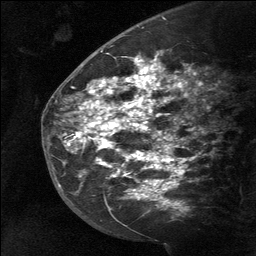
Breast MRI (dynamic contrast-enhanced), one sagittal slice; position 41 of 64 along the scan axis; dynamic contrast-enhanced study with each time point stored as its own series, time point 2 of 3 at this slice position (early post-contrast, ordered by acquisition time); 1.5 T; TE 4.8 ms, TR 27 ms; 2 mm slice thickness; 256 × 256 image matrix, field of view 180 × 180 mm. Female patient, age 39 years. Case-level facts recorded for this patient, not image findings: setting: breast cancer imaged before/during neoadjuvant chemotherapy; receptor status: HER2-positive.
Outlined on this slice (semi-automatic segmentation, software-assisted and operator-edited):
- analysis volume of interest (the breast-tissue region the enhancement analysis was run in; not a lesion): bounding box (x1, y1, x2, y2) in pixels: (58, 40, 184, 217)
- tumour enhancement mask (voxels above the 90 % enhancement threshold inside the analysis volume of interest): (67, 57, 177, 200)